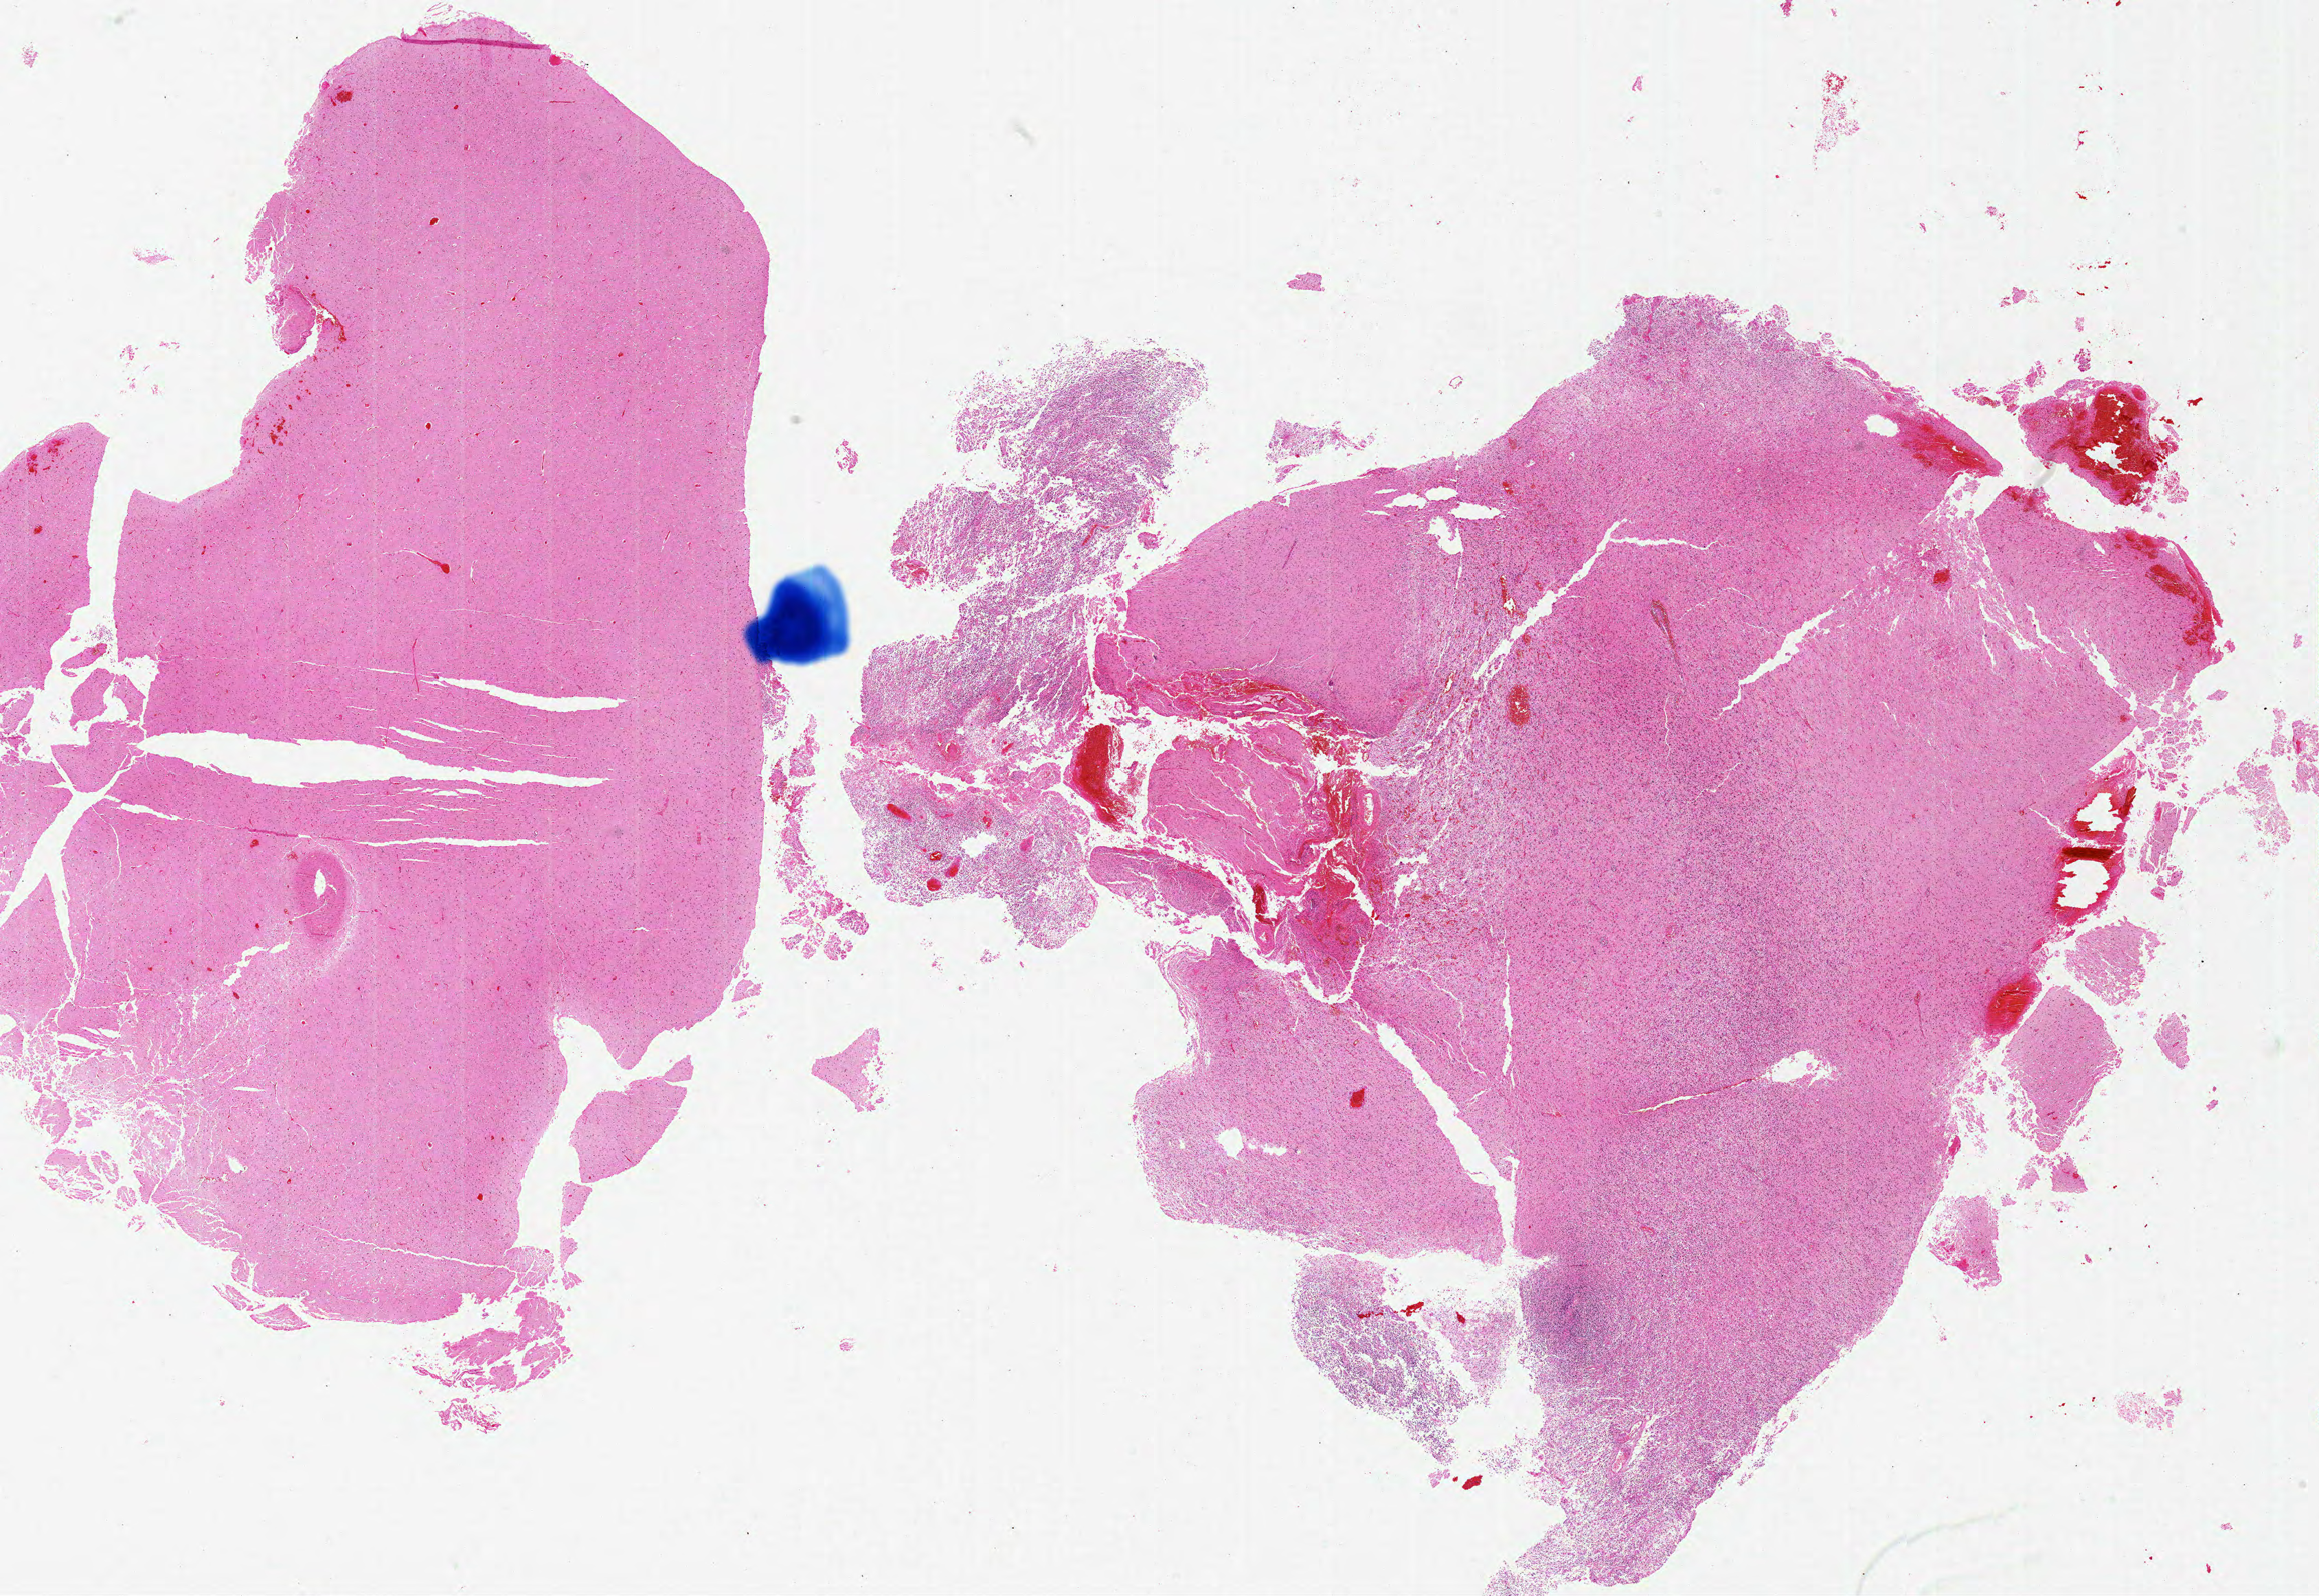
Whole-slide histology image, H&E-stained — whole scanned area (about 27.0 x 18.6 mm) shown as a low-resolution overview; formalin-fixed paraffin-embedded (FFPE) diagnostic section; primary tumour sample from the brain. Patient: female, age at initial diagnosis 36 years.
Histologic diagnosis: Glioblastoma.